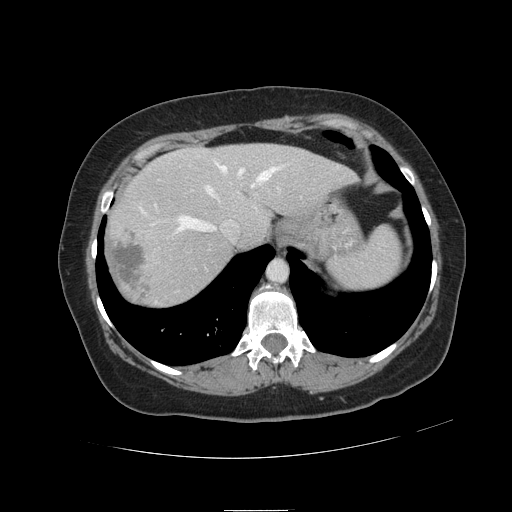
Contrast-enhanced abdominal CT, one axial slice. Position 95 of 121 along the scan axis. 120 kVp. Soft-tissue window (W 400 / L 40 HU). 2.5 mm slice thickness. 512 × 512 image matrix, field of view 400 × 400 mm. Female patient, age 52 years. Case-level facts recorded for this patient, not image findings: diagnosis: colorectal cancer liver metastases, imaged before liver resection; multiple liver metastases: yes; largest metastasis: 6.3 cm; chemotherapy before resection: yes.
Structures marked on this image (outlined manually by an expert reader):
- hepatic veins: box from (x=140, y=162) to (x=279, y=232) px
- liver: (x=105, y=144)–(x=354, y=308)
- planned liver remnant (the part of the liver to remain after resection): (x=169, y=144)–(x=353, y=244)
- portal vein (with intrahepatic branches): (x=154, y=188)–(x=280, y=207)
- liver metastasis: (x=110, y=226)–(x=151, y=296)